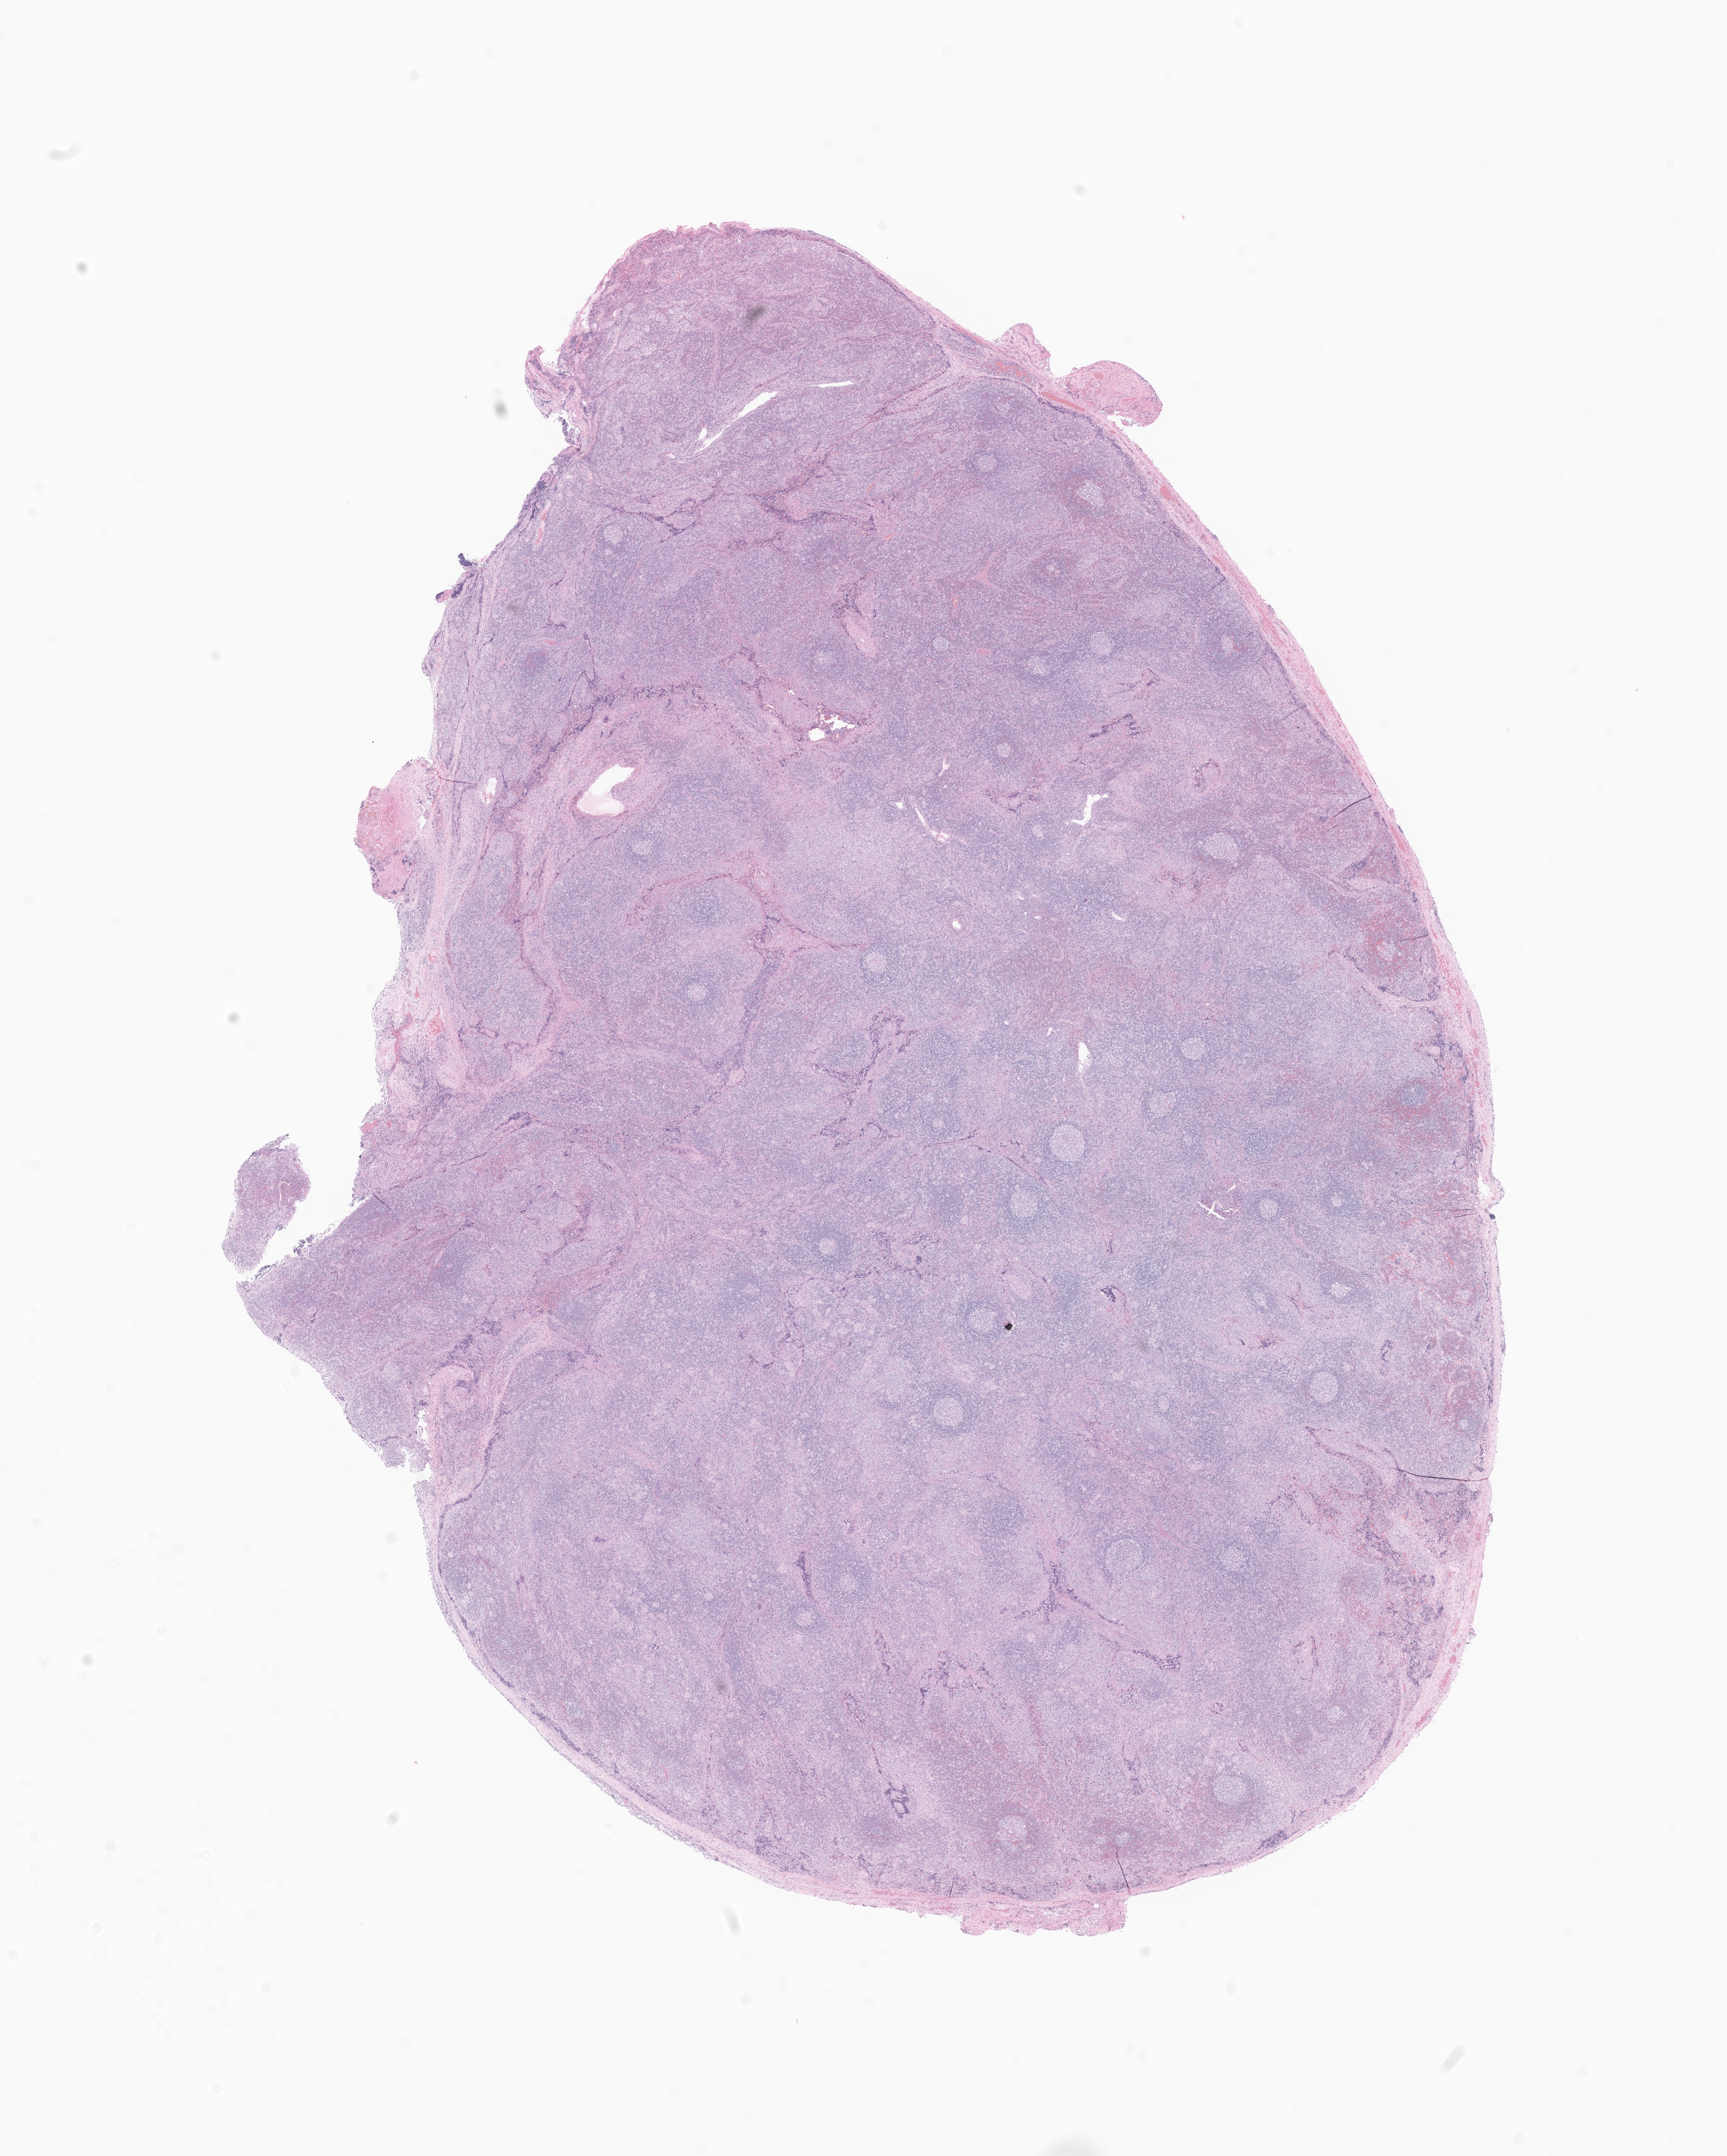
H&E whole-slide image of tumor tissue from the head and neck lymph node, a low-resolution overview of the entire scanned area, about 14.6 x 18.3 mm, formalin-fixed paraffin-embedded section. Patient male; age 176 months (14 years 8 months).
Tissue or organ of origin (case record): lymph nodes of head, face and neck. Recorded diagnosis: Malignant lymphoma, non-Hodgkin, NOS.